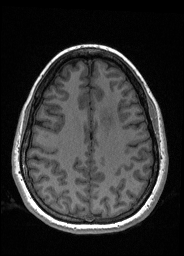
Pre-operative brain MRI before brain-tumour surgery, one axial slice; T1-weighted post-contrast; 1 mm slice thickness; 184 × 256 image matrix, field of view 180 × 250 mm. From the clinical record (not read from this slice): histopathology: Oligodendroglioma; WHO grade: 2; IDH mutation: yes; tumour location: Left Frontal.
Outlined on this slice (manually delineated by an expert):
- tumour: box from (x=100, y=106) to (x=117, y=127) px